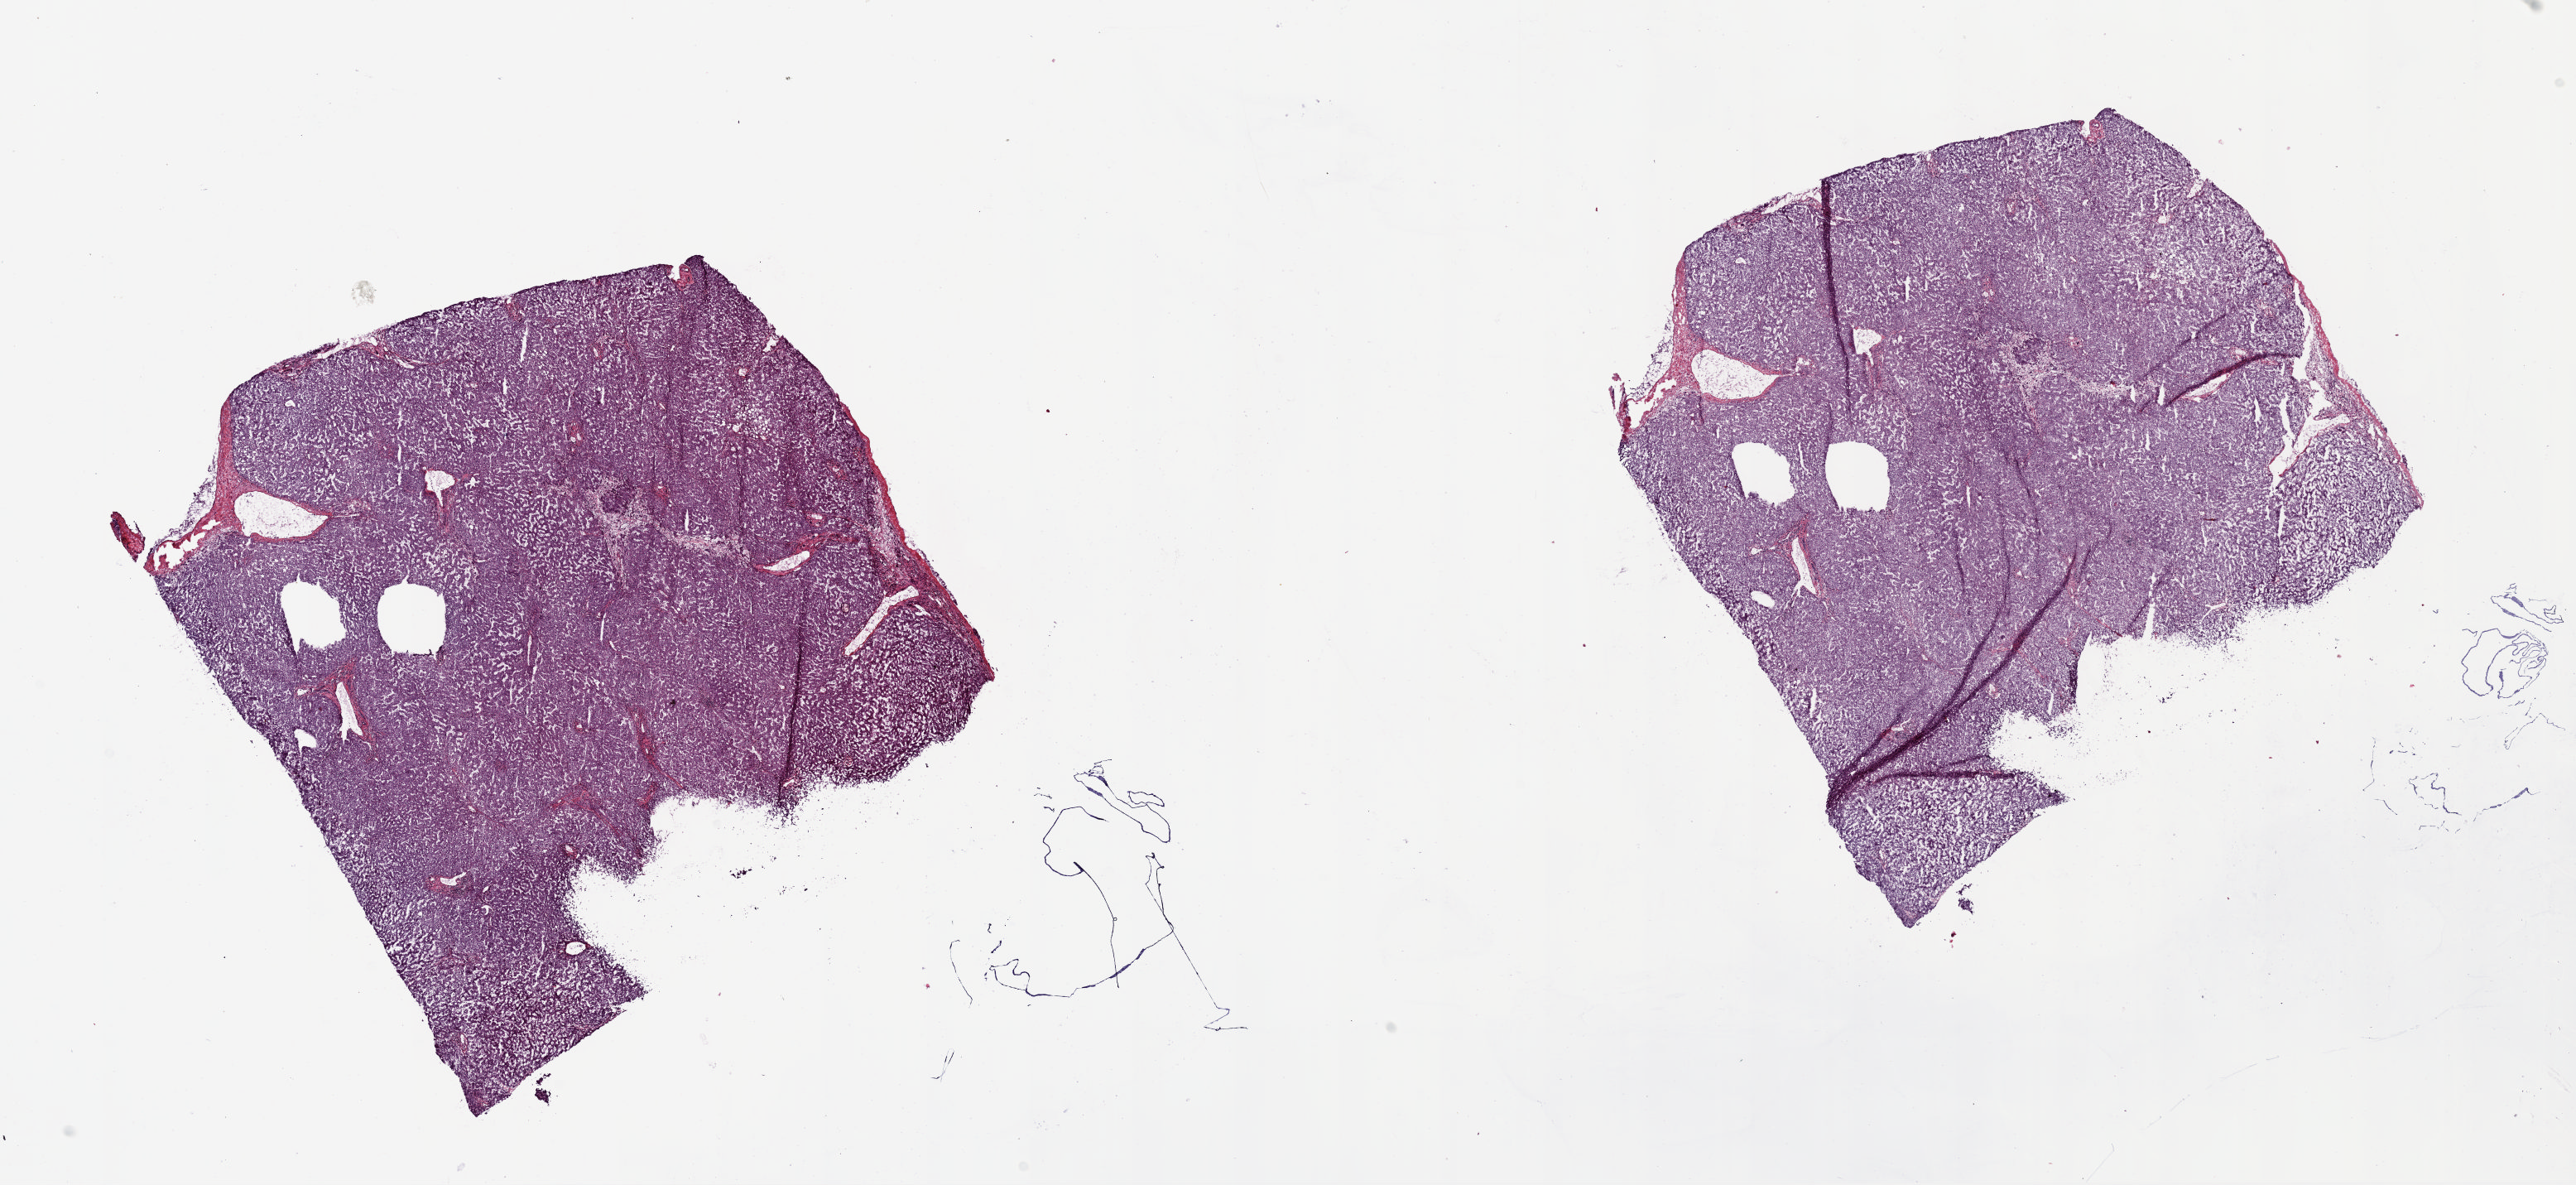
Digitized H&E-stained tissue section (whole slide) — whole scanned area (about 24.5 x 11.3 mm, acquisition: 20x scan) shown as a low-resolution overview, frozen section from the top of the tissue portion, liver, solid tissue normal (non-tumour tissue) sample. Female patient; age at initial diagnosis 65 years. Pathologist review of this section (percent, as recorded): tumour cells 0%, tumour nuclei 0%, normal cells 100%, stromal cells 0%, necrosis 0%. Infiltration values recorded for this section: lymphocyte infiltration 3%, monocyte infiltration 4%, neutrophil infiltration 0%.
This section: solid tissue normal sample (biorepository sample class). Patient diagnosis: Hepatocellular carcinoma, NOS.